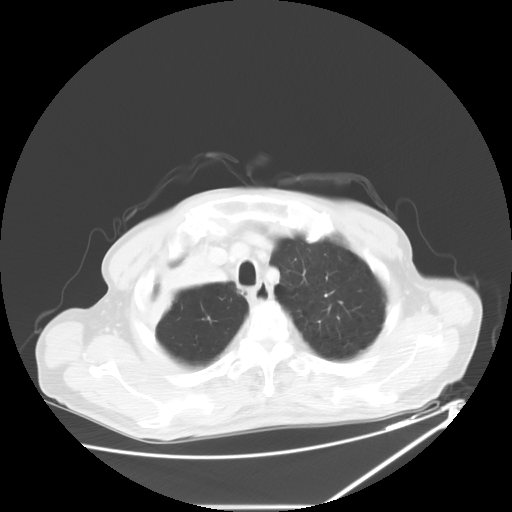
Chest CT, one axial slice. Slice 52 of 60 in the series (ordered by position). Reconstruction kernel STANDARD. Lung window (W 1500 / L -600 HU). 5 mm slice thickness. 512 × 512 image matrix, field of view 410 × 410 mm. Patient: male, 73 years. From the clinical record (not read from this slice): clinical TNM (as recorded): T2a N1 M0.
Outlined on this slice (rectangle marked by the reading radiologist):
- lung tumour (recorded histology: squamous cell carcinoma): bounding box <145,255,234,344> (left, top, right, bottom; pixels)